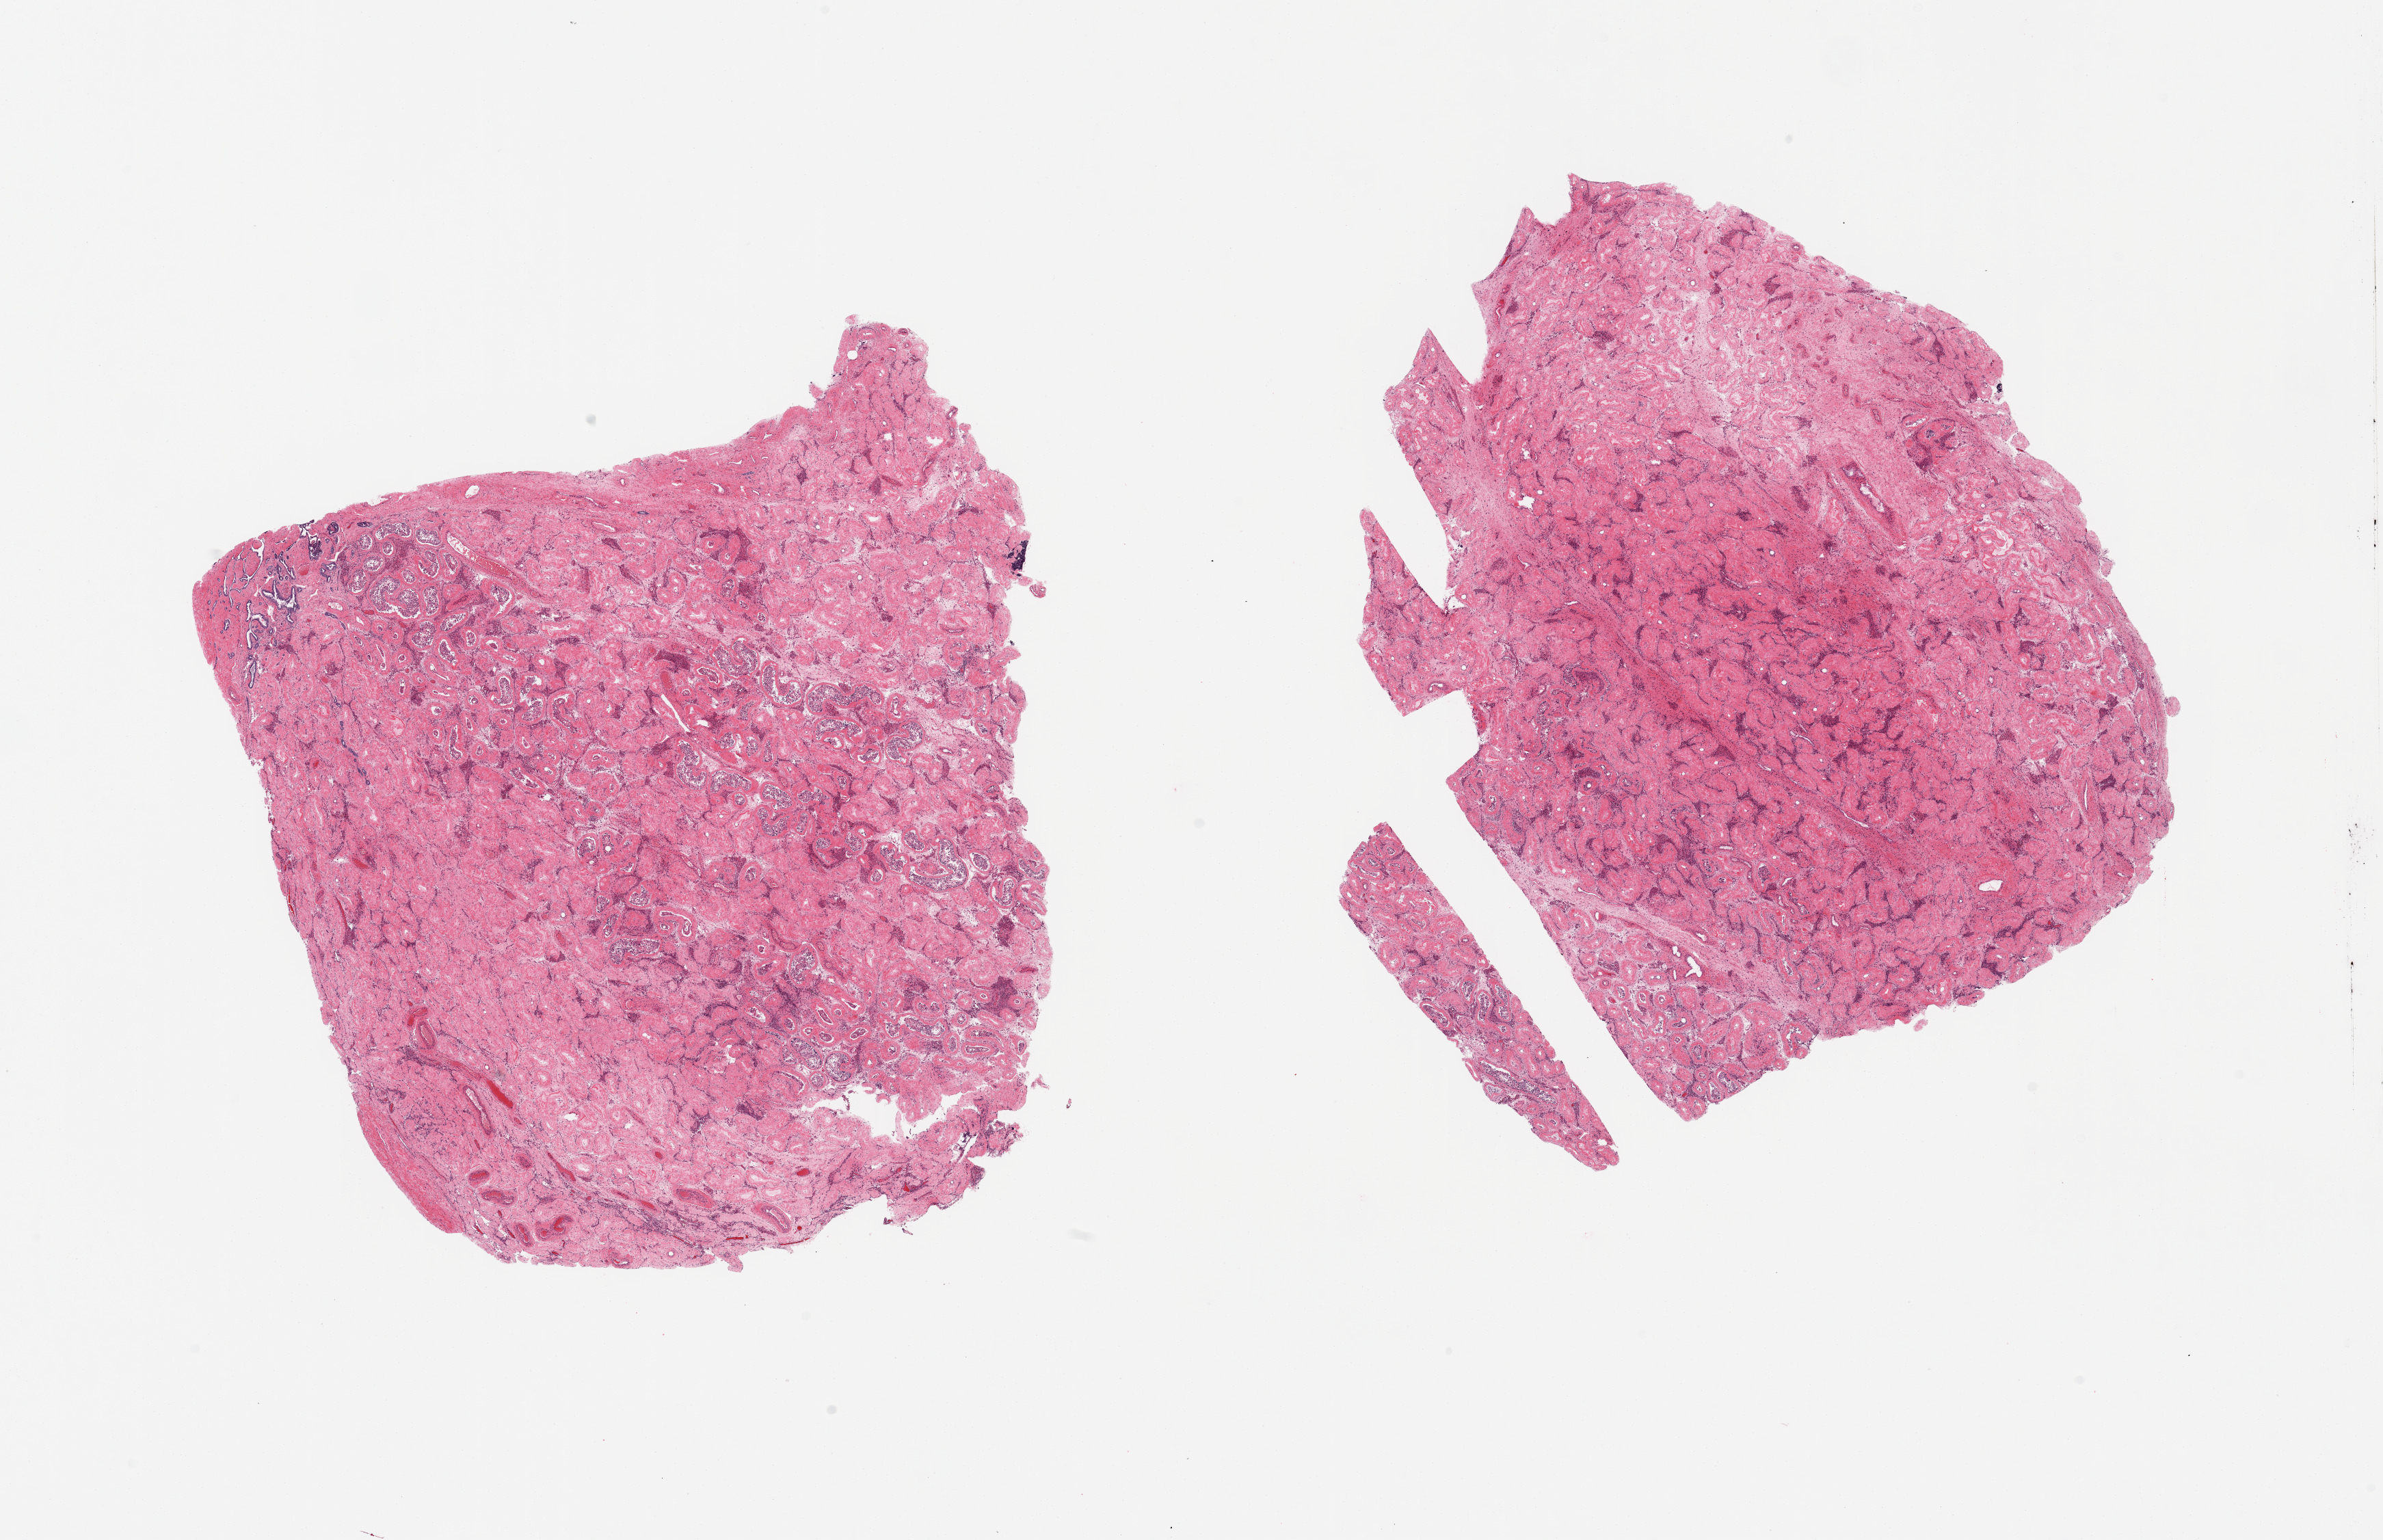
Whole-slide image, H&E stain, a low-resolution overview of the entire scanned area, about 27.6 x 17.8 mm (from a 20x scan), PAXgene-fixed paraffin-embedded (PFPE) section, sampled site (target tissue): testis, tissue donor sample. Male donor.
Pathologist's review note for this sample: 2 pieces; sclerosis of tubules with only focal residual spermatogenesis, portion of rete testis.